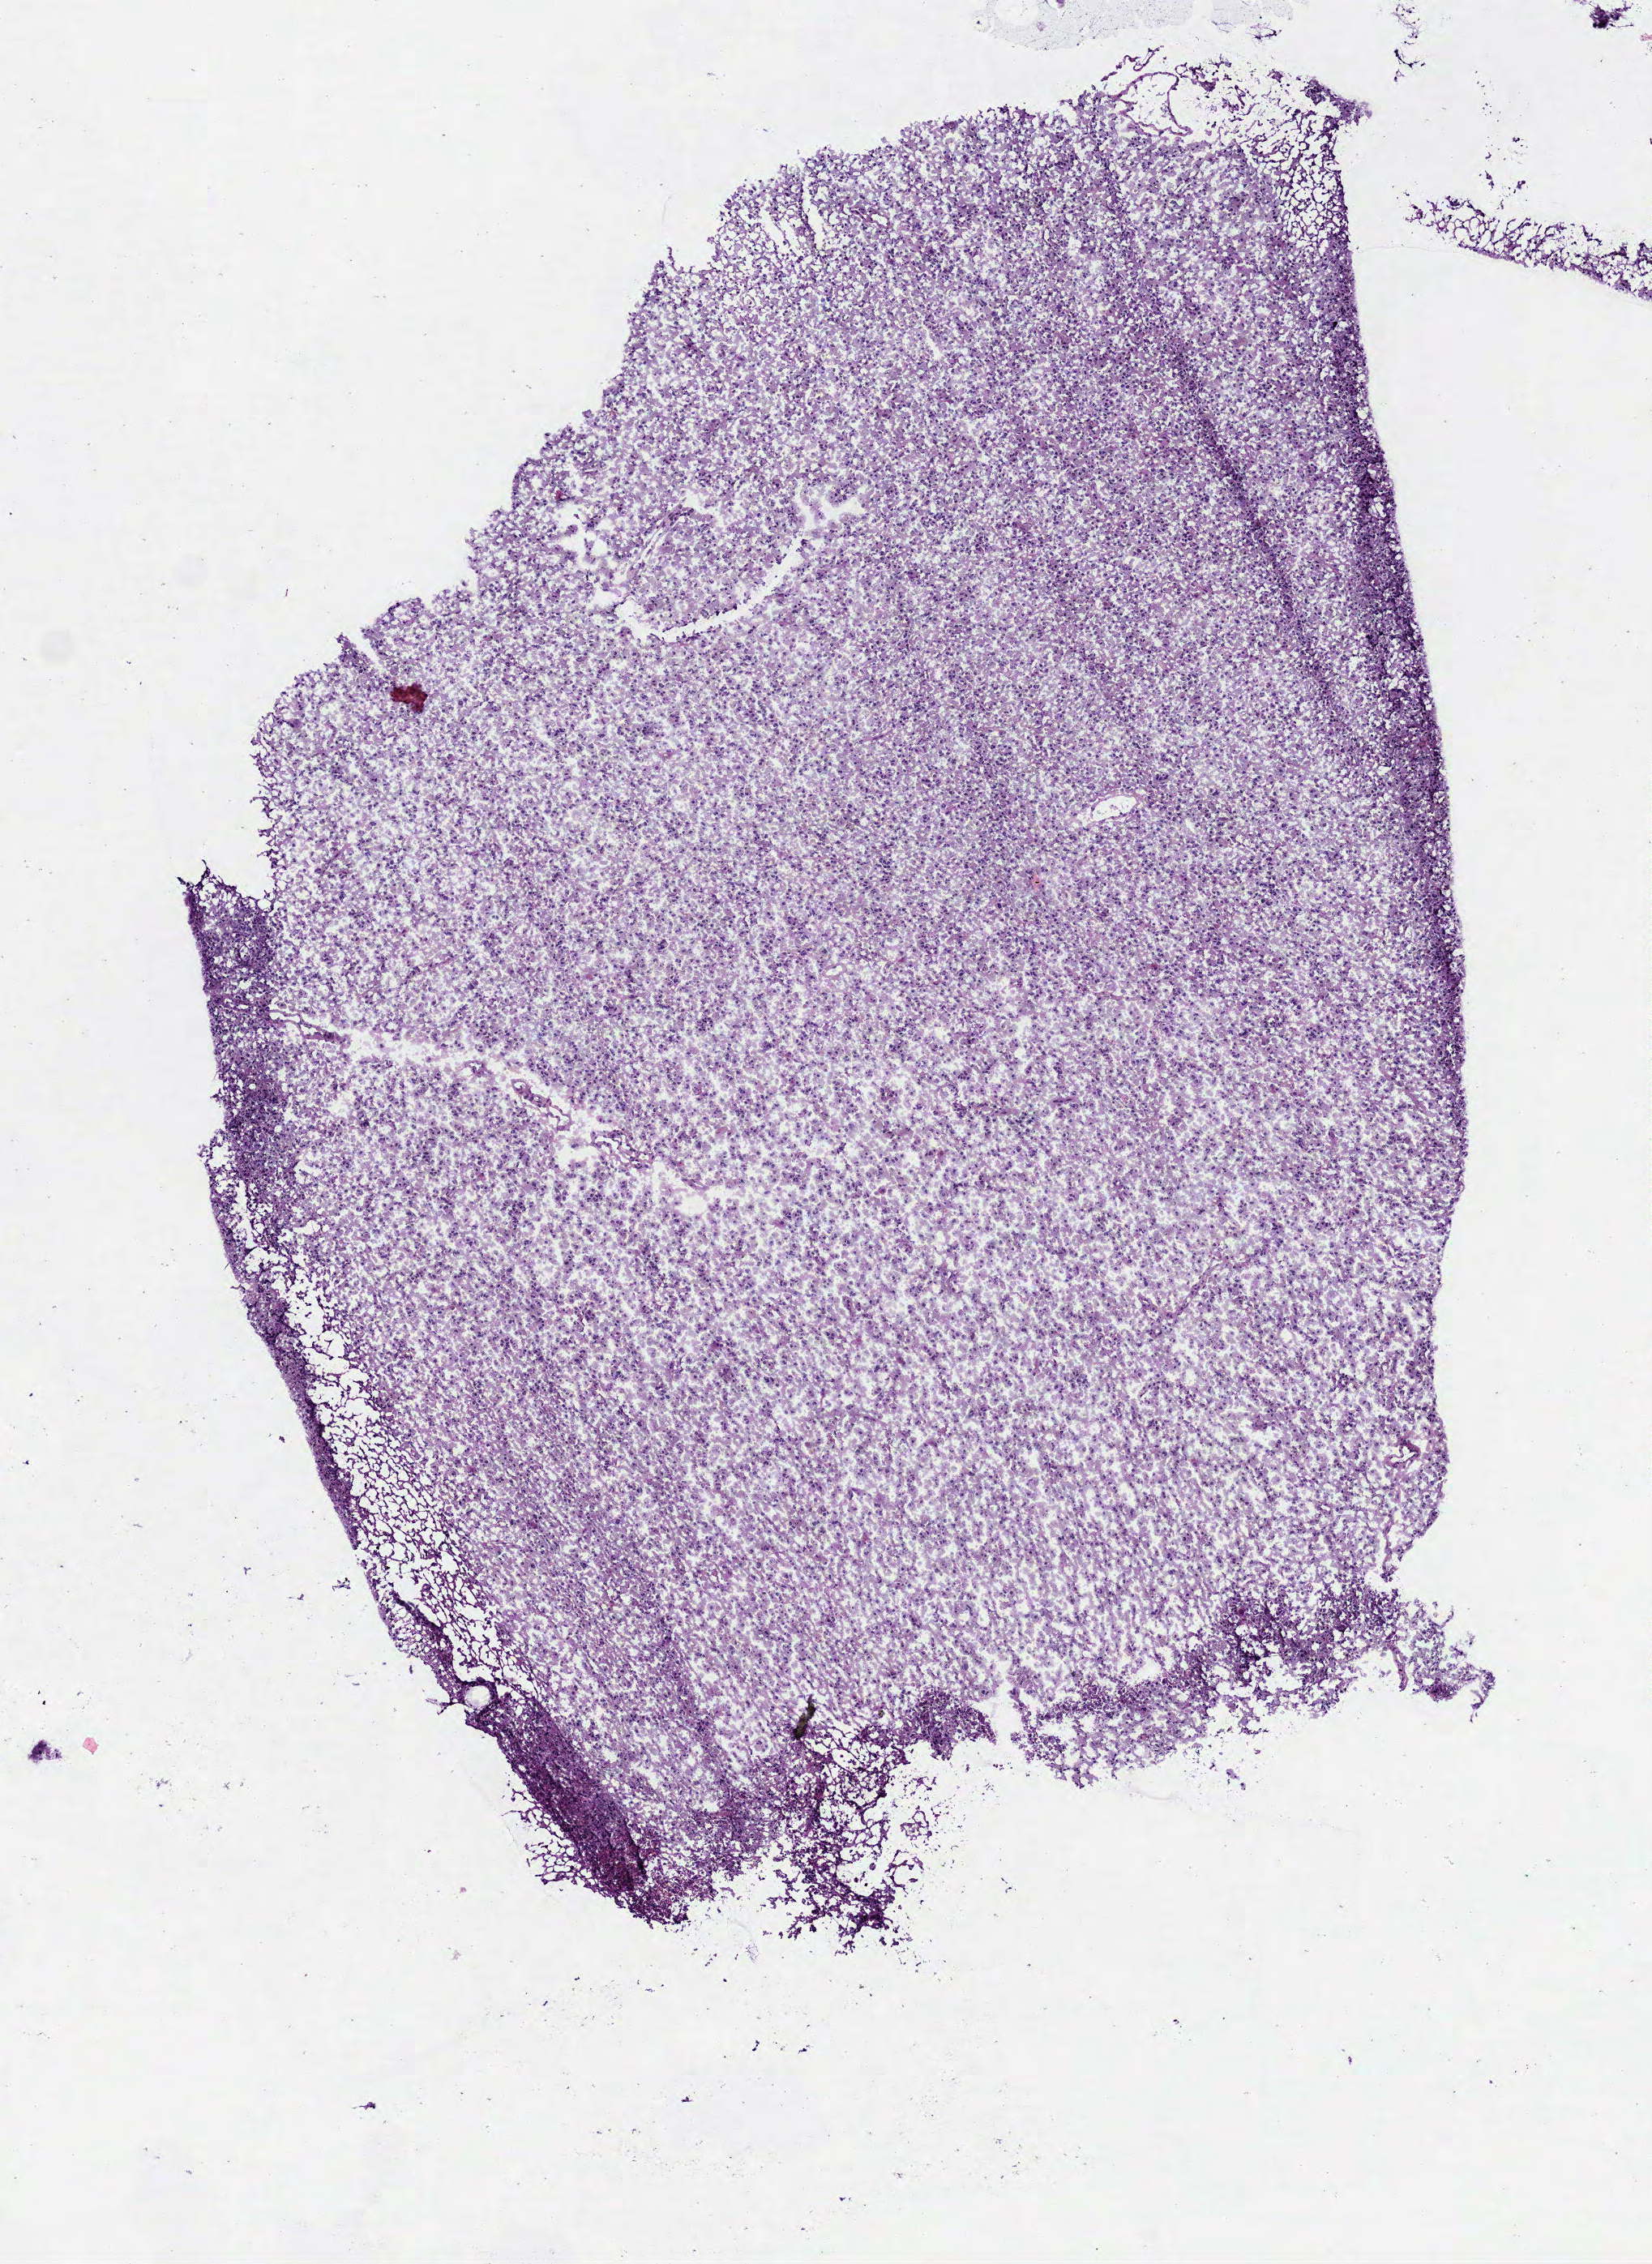
H&E whole-slide image, low-resolution overview of the scanned area, about 4.1 x 5.6 mm (from a 40x scan), frozen section from the bottom of the tissue portion, brain, primary tumour sample. Male, age 56 years at initial diagnosis. Histologic grade: G2 (moderately differentiated). Composition of this section per pathologist review: tumour cells 100%, tumour nuclei 80%, normal cells 0%, stromal cells 0%, necrosis 0%.
Pathologic diagnosis: Oligodendroglioma, NOS (cerebrum). Laterality: left.